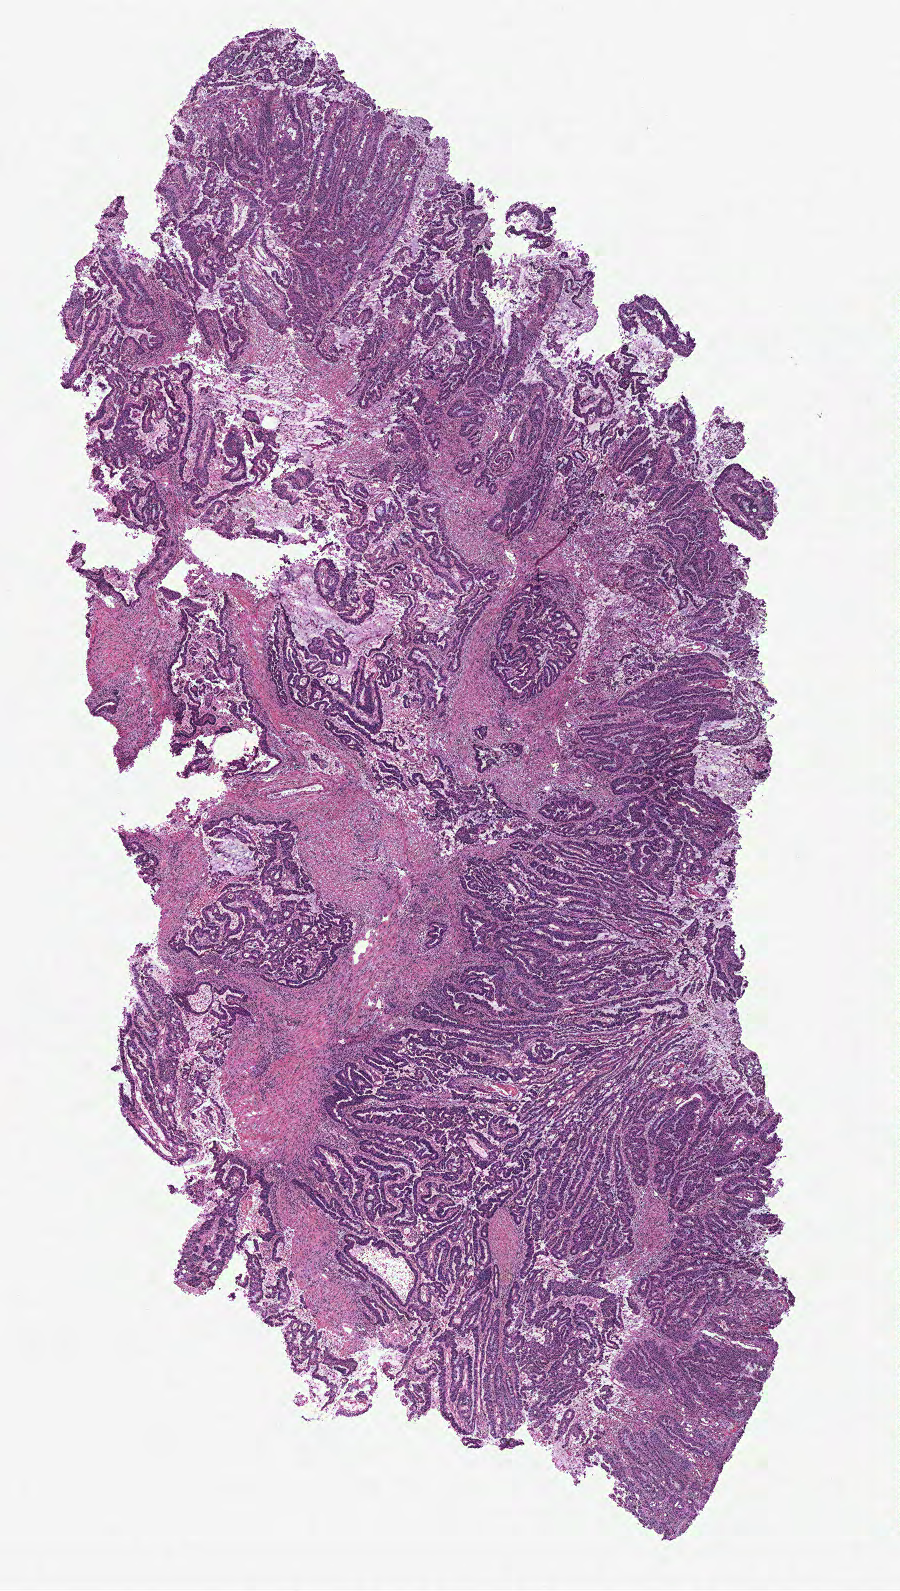
Whole-slide histology image, H&E — low-resolution overview of the scanned area, about 7.2 x 12.7 mm (acquisition: 40x scan), tumour tissue sample, colon. 71-year-old female patient.
AJCC pathologic stage: IIB. Histologic diagnosis: Adenocarcinoma, NOS. Primary tumour site (as recorded): colon.